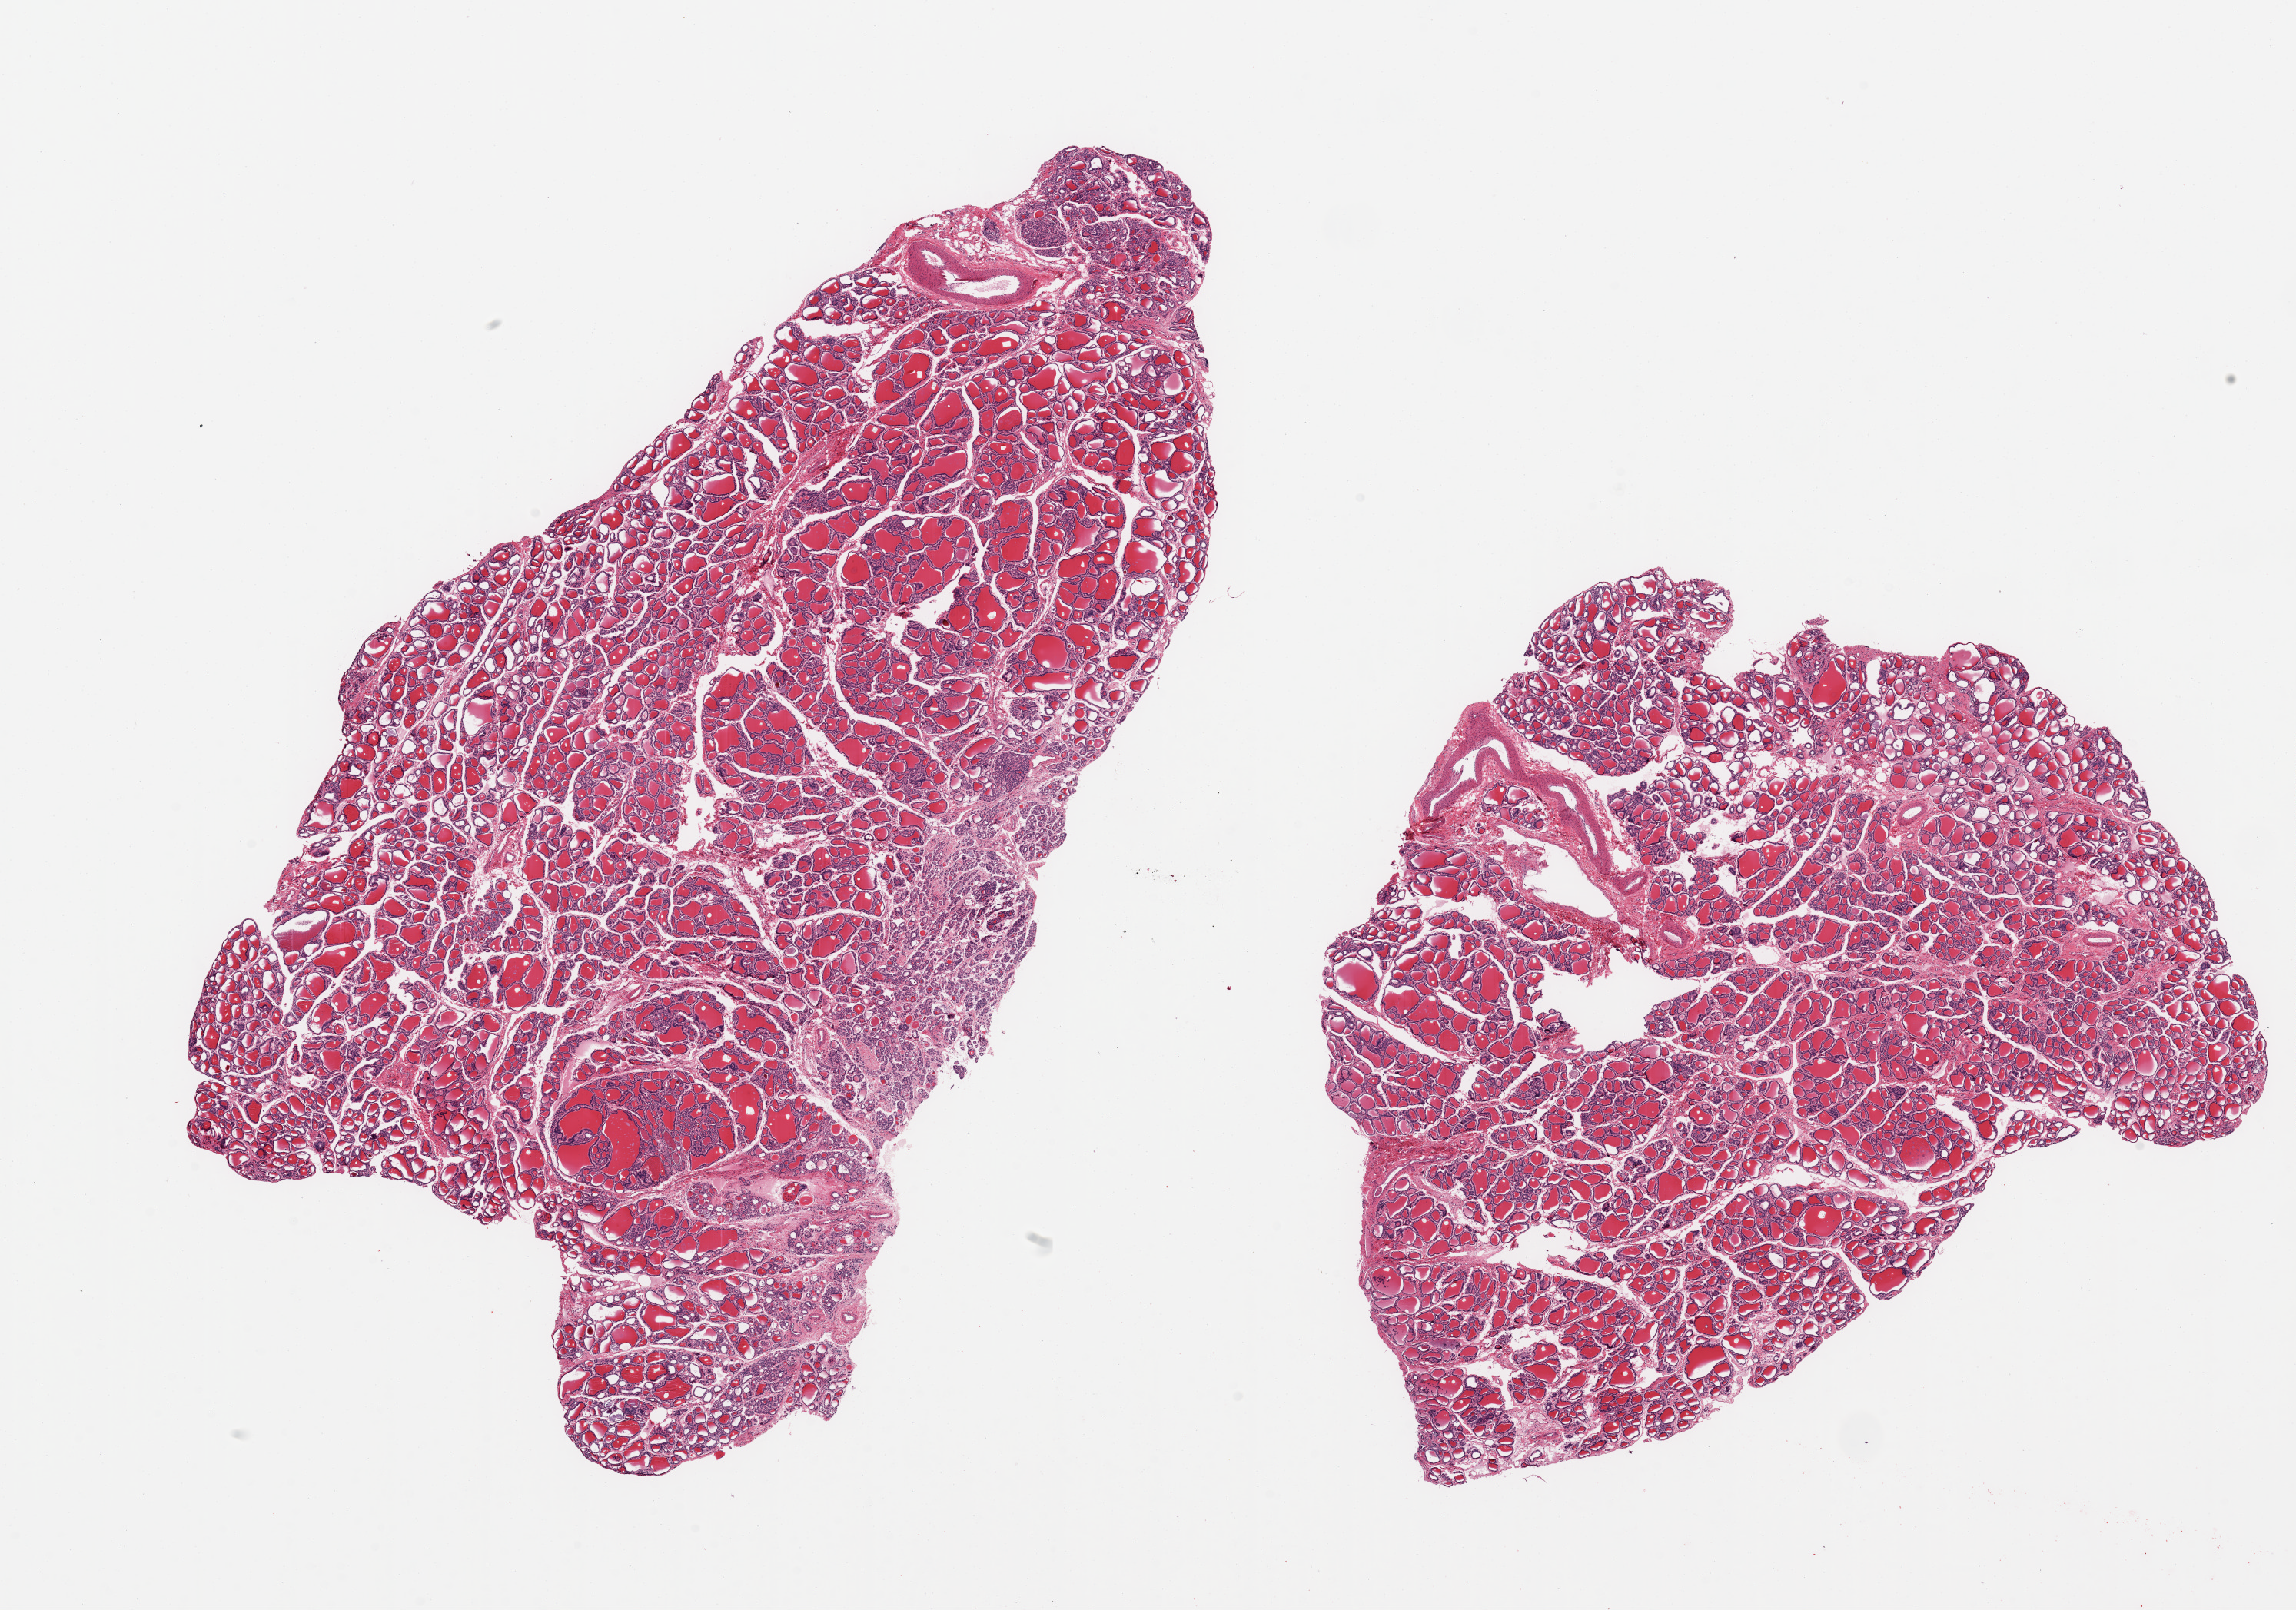
Hematoxylin and eosin (H&E) whole-slide image — low-resolution overview of the scanned area, about 23.6 x 16.6 mm (from a 20x scan). PAXgene-fixed, paraffin-embedded tissue. Section of thyroid (target tissue). Tissue donor sample.
Pathologist's review note for this sample: 2 pieces; mild nodular hyperplasia.